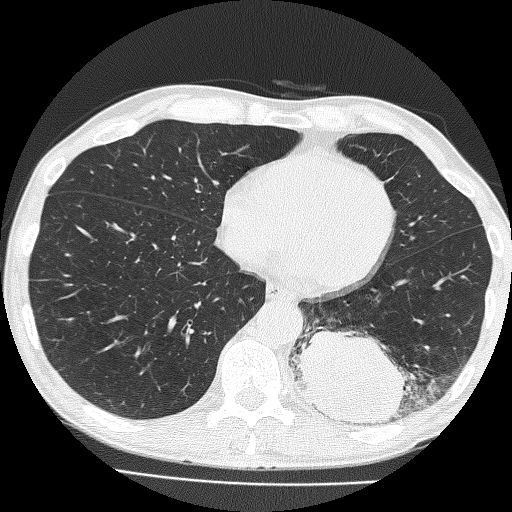
Low-dose screening chest CT, one axial slice. Slice 58 of 160 in the series (ordered by position). Lung window (W 1500 / L -600 HU). 2 mm slice thickness. 512 × 512 image matrix, field of view 324 × 324 mm.
Annotated regions visible in this slice (manually delineated by an expert):
- lesion 1 (tumor, lower lobe of left lung): bounding box <294,329,407,426> (left, top, right, bottom; pixels)